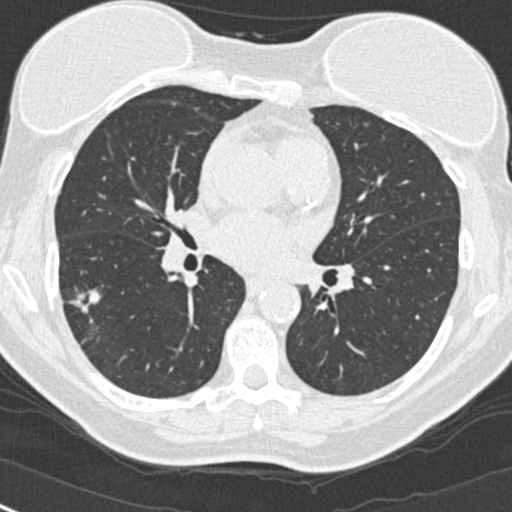
Low-dose screening chest CT, one axial slice; position 136 of 268 along the scan axis; 120 kVp; lung window (W 1500 / L -600 HU); 512 × 512 image matrix, field of view 296 × 296 mm.
Outlined on this slice (outlined manually by an expert reader):
- lesion 1 (tumor, upper lobe of right lung): bounding box [x1, y1, x2, y2] px = [68, 289, 102, 313]